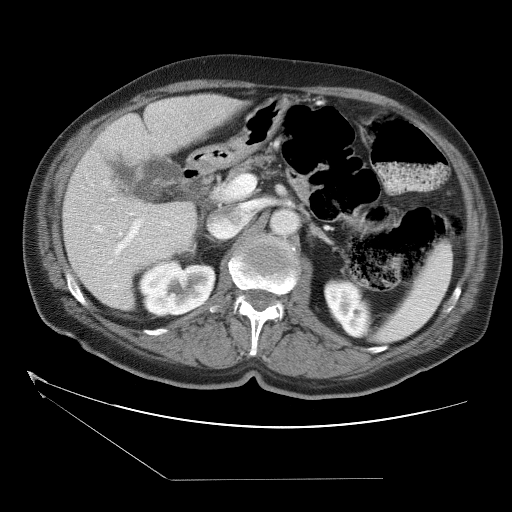
Contrast-enhanced abdominal CT (liver protocol), one axial slice. Slice 15 of 38 in the series (ordered by position). One of 2 acquisitions stored at this slice position. Soft-tissue window (W 400 / L 40 HU). 5 mm slice thickness. 512 × 512 image matrix, field of view 400 × 400 mm. Case-level facts recorded for this patient, not image findings: diagnosis: hepatocellular carcinoma (patient treated with transarterial chemoembolisation; whether this scan precedes or follows treatment is not stated here); TNM stage (as recorded): Stage-II; Child-Pugh class: A; tumour nodularity: multinodular; tumour size: 0.8 cm.
Annotated regions visible in this slice (semi-automatic segmentation, software-assisted and operator-edited):
- liver parenchyma outside the tumour (the mass and vessels are separate outlines, so this box may not span the whole liver): box from (x=62, y=94) to (x=247, y=310) px
- liver vessels: (x=93, y=219)–(x=143, y=264)